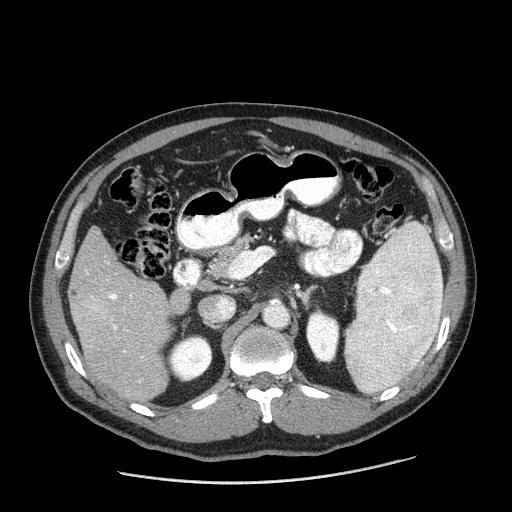
Contrast-enhanced abdominal CT (liver protocol), one axial slice; position 89 of 198 along the scan axis; reconstruction kernel STANDARD; 120 kVp; one of 2 acquisitions stored at this slice position; soft-tissue window (W 400 / L 40 HU); 2.5 mm slice thickness; 512 × 512 image matrix. From the clinical record (not read from this slice): diagnosis: hepatocellular carcinoma (patient treated with transarterial chemoembolisation; whether this scan precedes or follows treatment is not stated here); TNM stage (as recorded): Stage-II; Child-Pugh class: A; tumour differentiation: moderately differentiated; tumour size: 2.6 cm.
Outlined on this slice (semi-automatic segmentation, software-assisted and operator-edited):
- liver parenchyma outside the tumour (the mass and vessels are separate outlines, so this box may not span the whole liver): bounding box [x1, y1, x2, y2] px = [68, 226, 190, 400]
- mass: [68, 288, 105, 316]
- liver vessels: [86, 272, 132, 353]